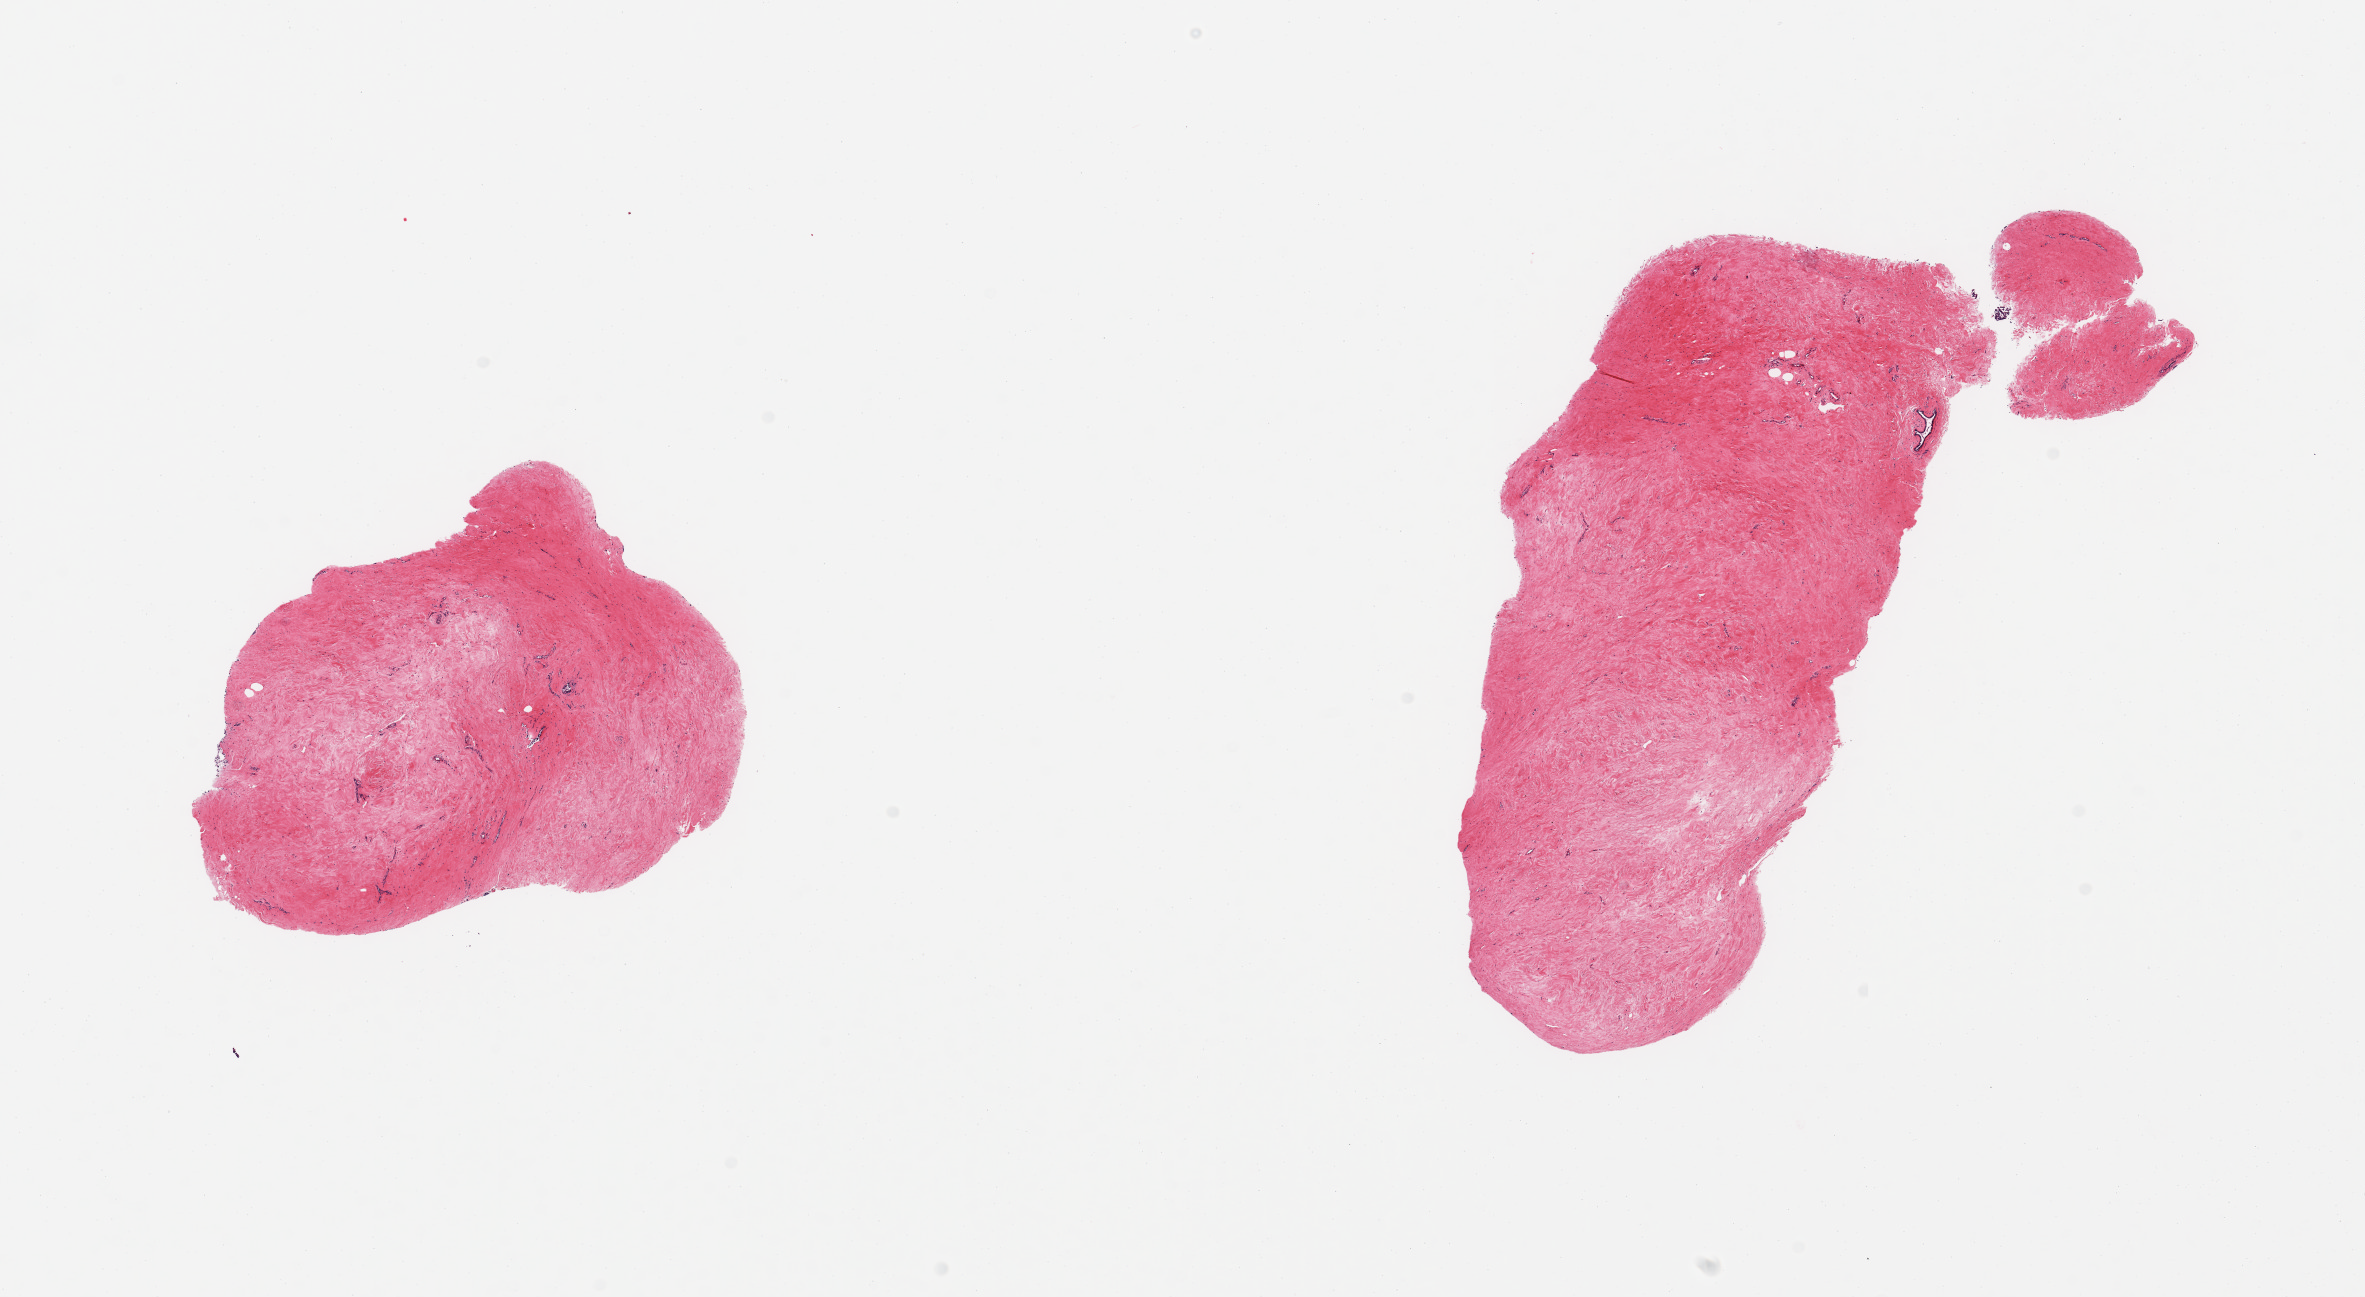
Digitized H&E-stained section — shown as a low-resolution overview of the whole scanned area (about 18.7 x 10.3 mm, acquisition: 20x scan); PAXgene-fixed paraffin-embedded (PFPE) section; sampled site (target tissue): breast; donor tissue sample.
• review note (as recorded): 2 pieces; dense fibrous stroma and ductal structures consistenet with gynecomastoid stromal and ductal hyperplasia